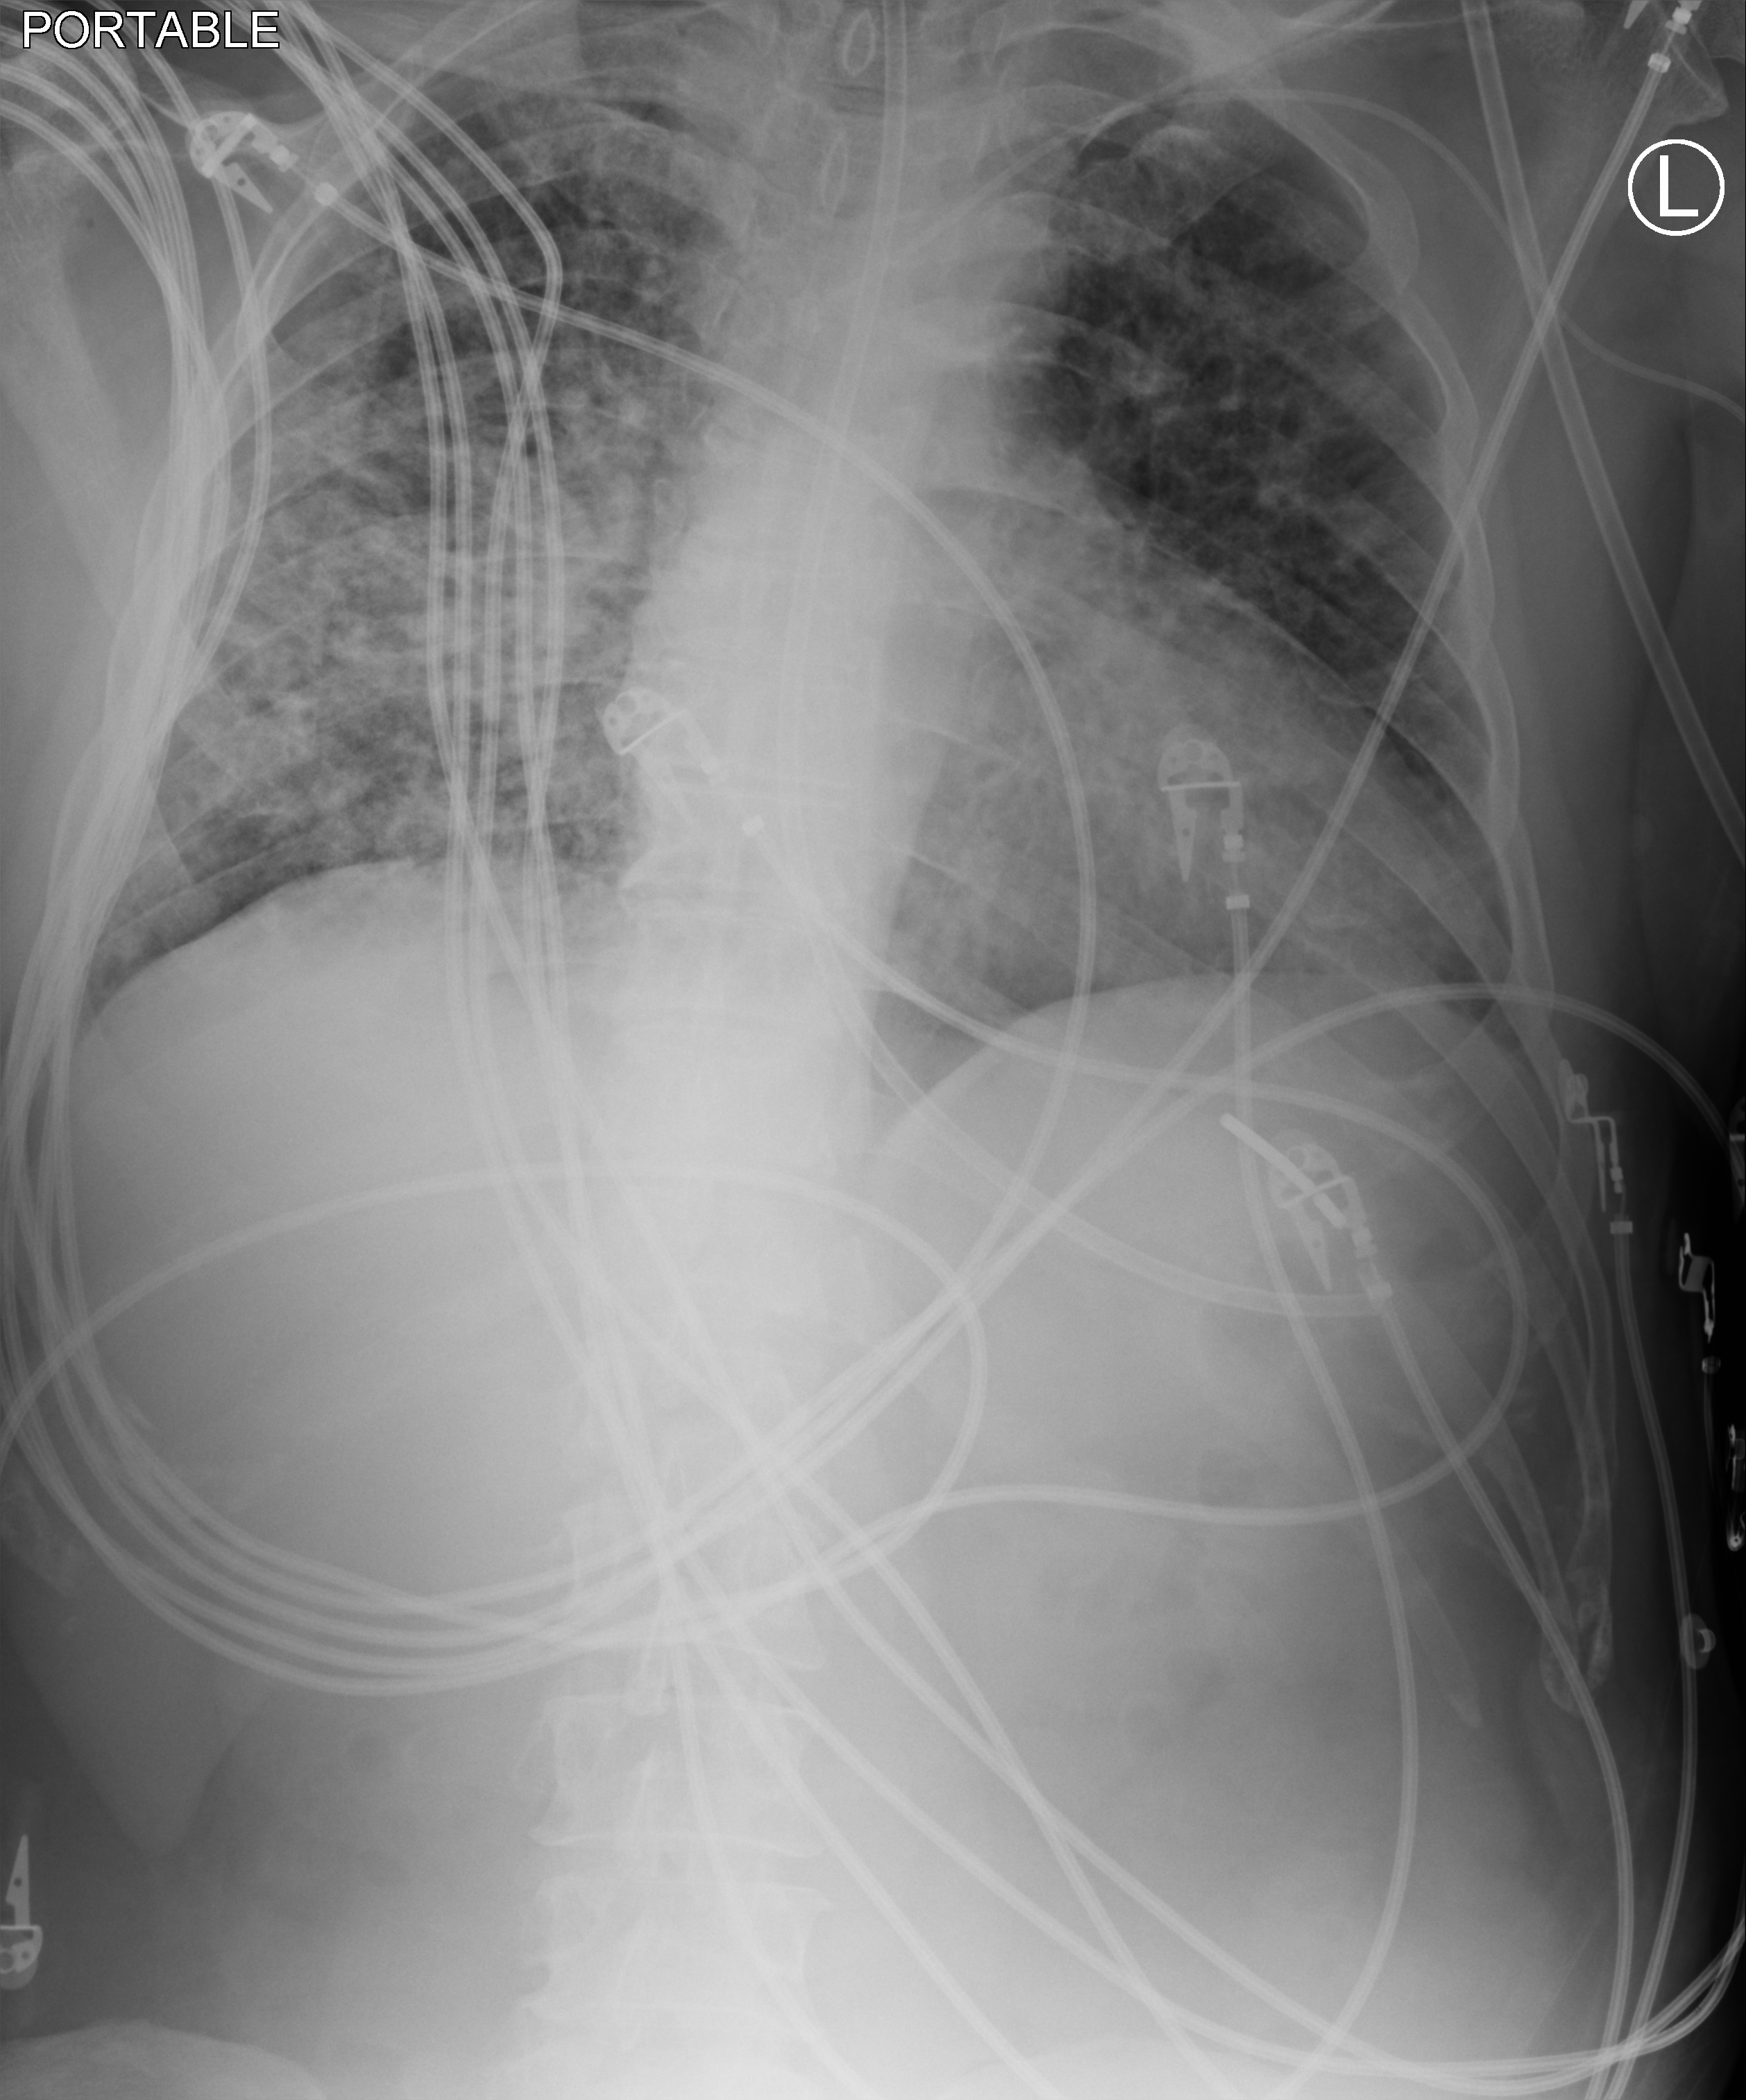
Bedside chest radiograph (computed radiography); anteroposterior (AP) projection. Patient hospitalised with COVID-19; male, aged 18–59 years.
Admission-level facts for this patient (not findings on this image; timing relative to this image not recorded): mechanically ventilated during this hospital stay: yes; admitted to intensive care during this hospital stay: yes; other chronic lung disease (admission record): no.